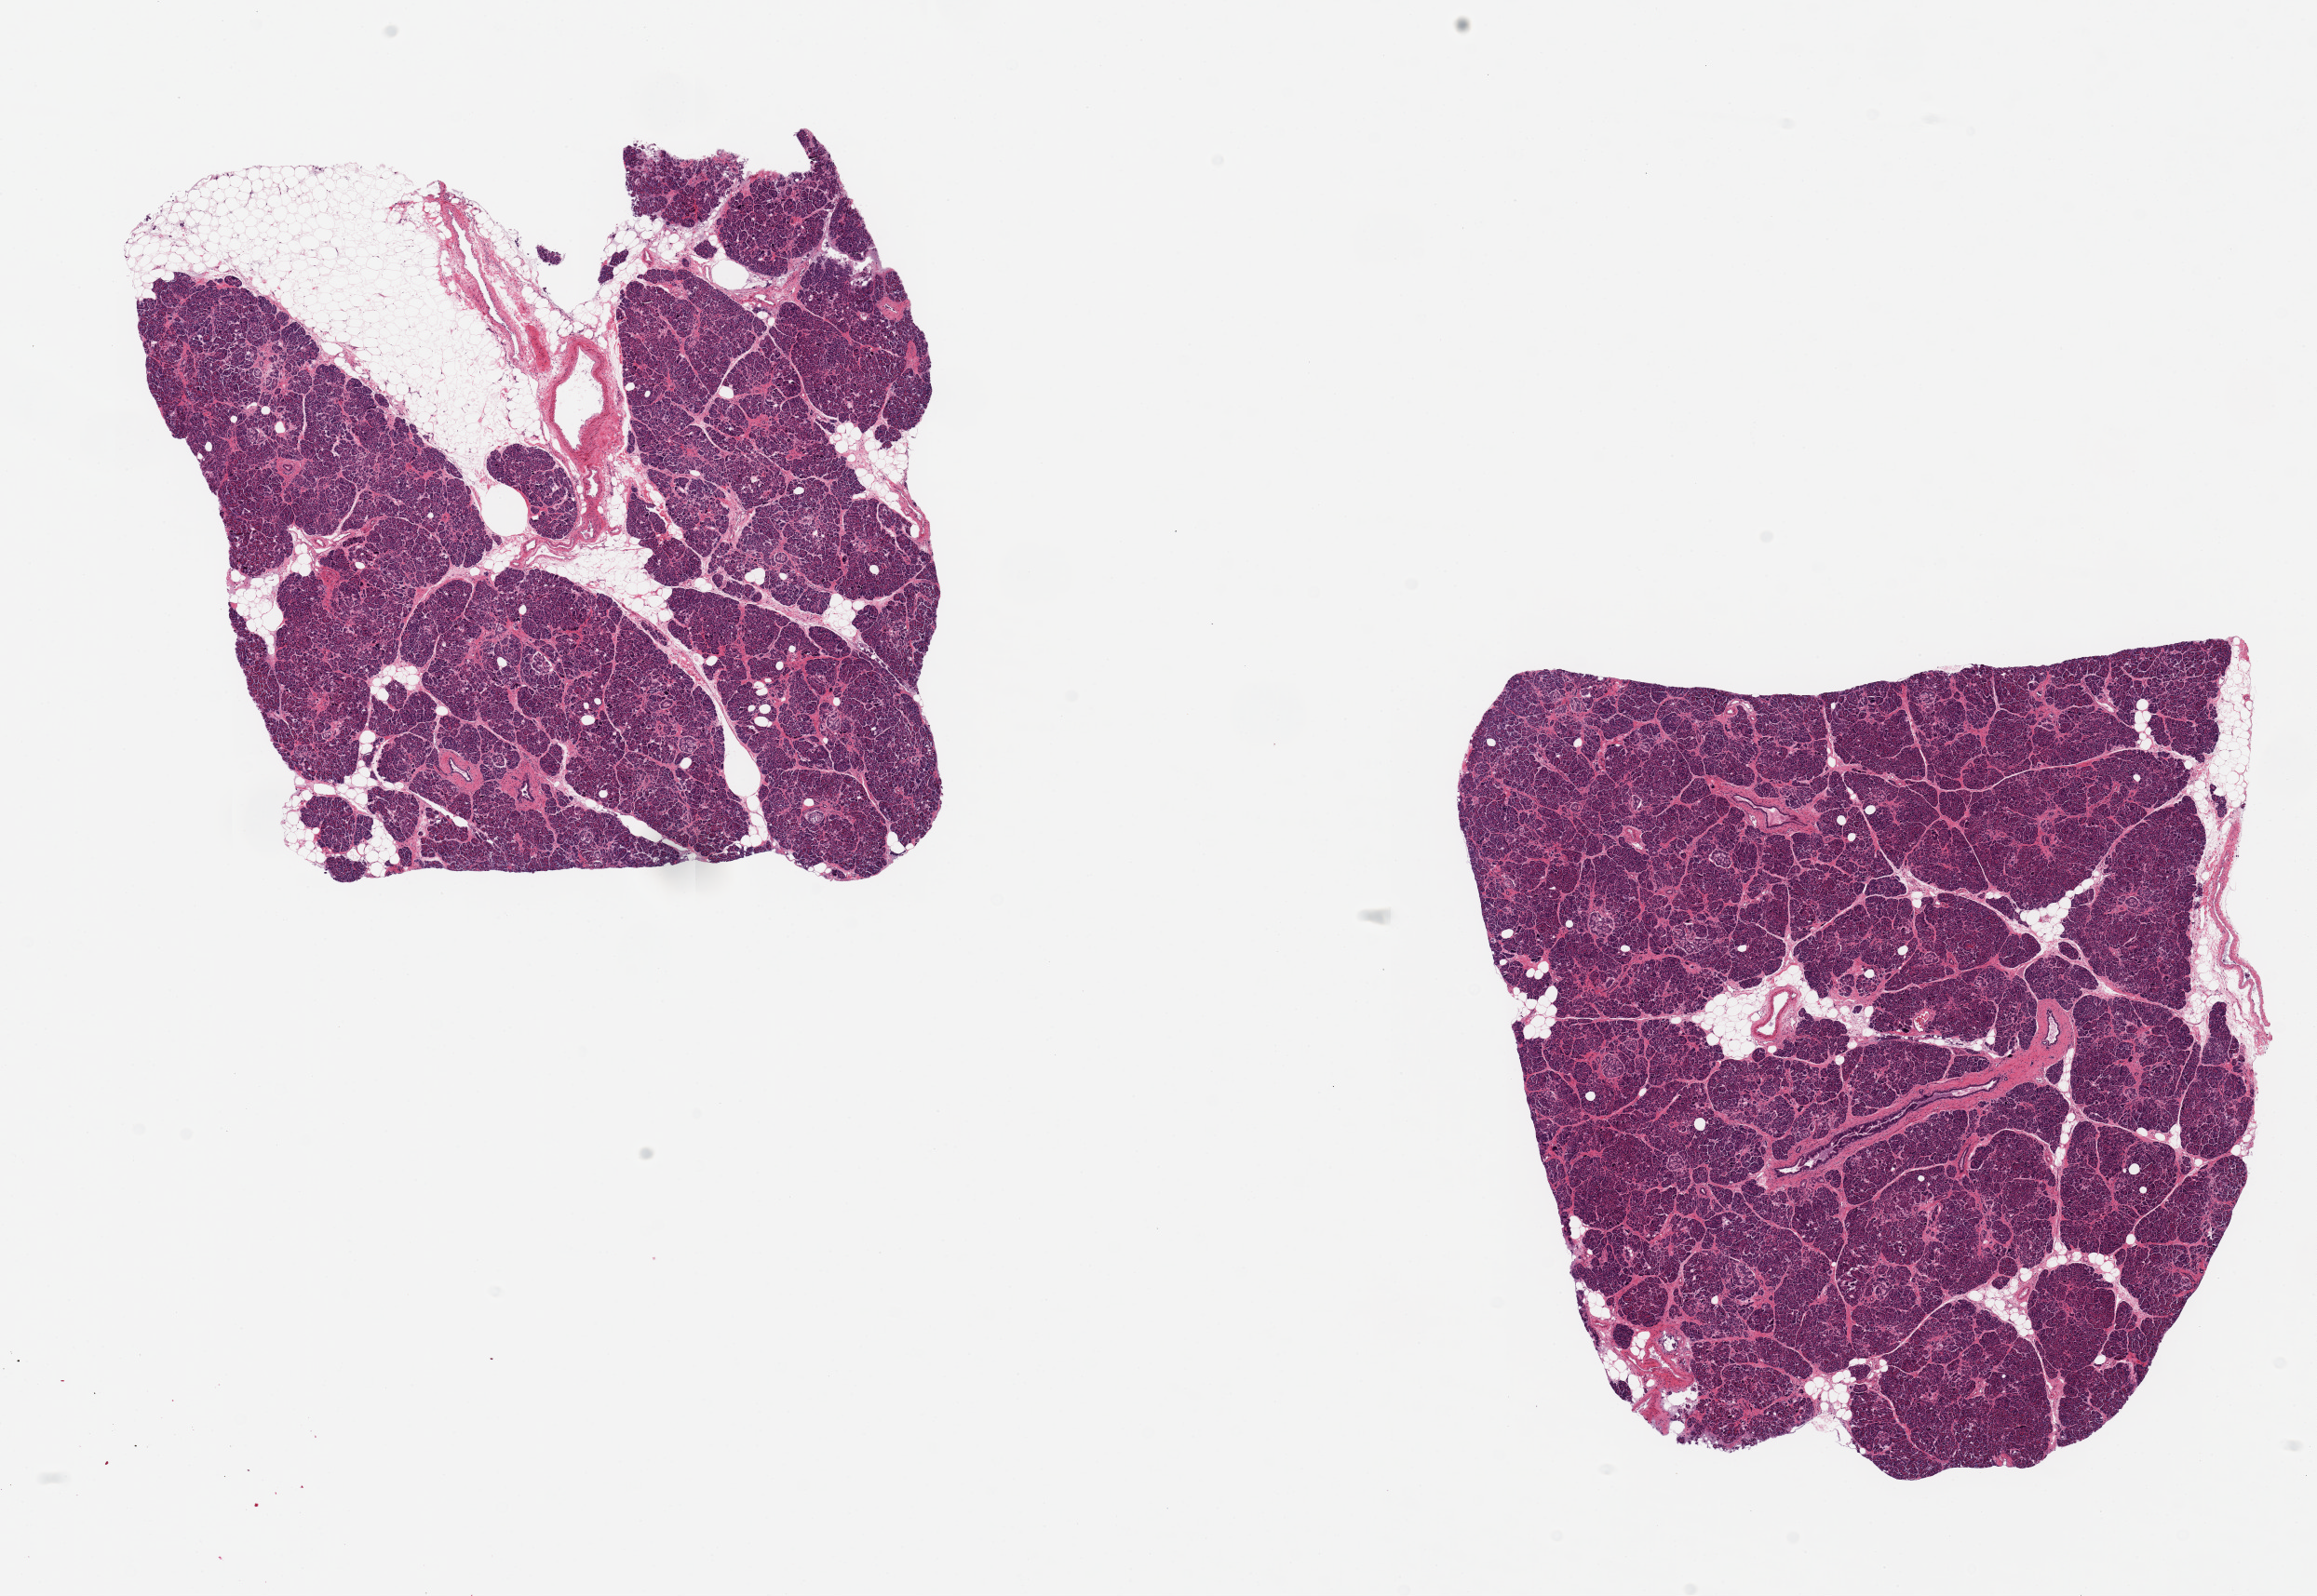
Whole-slide image, haematoxylin and eosin stain — low-resolution overview of the scanned area, about 19.7 x 13.6 mm (from a 20x scan), PAXgene-fixed, paraffin-embedded tissue, section of pancreas (target tissue), donor tissue sample.
Reviewer comment on this tissue sample: 2 pieces 7x6mm; Remarkably well preserved, ~20% interstitial/adherent fat; Islets well preserved.